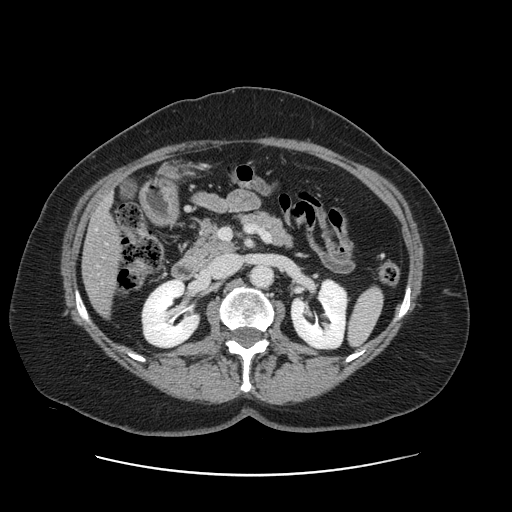
Contrast-enhanced abdominal CT, one axial slice. Slice 58 of 161 in the series (ordered by position). Intravenous contrast given. Soft-tissue window (W 400 / L 40 HU). 2.5 mm slice thickness. 512 × 512 image matrix, field of view 398 × 398 mm. Female patient, age 62 years. Case-level facts recorded for this patient, not image findings: diagnosis: colorectal cancer liver metastases, imaged before liver resection; multiple liver metastases: no; largest metastasis: 2.5 cm; chemotherapy before resection: yes.
Annotated regions visible in this slice (manually delineated by an expert):
- liver: bounding box [x1, y1, x2, y2] px = [83, 199, 119, 313]